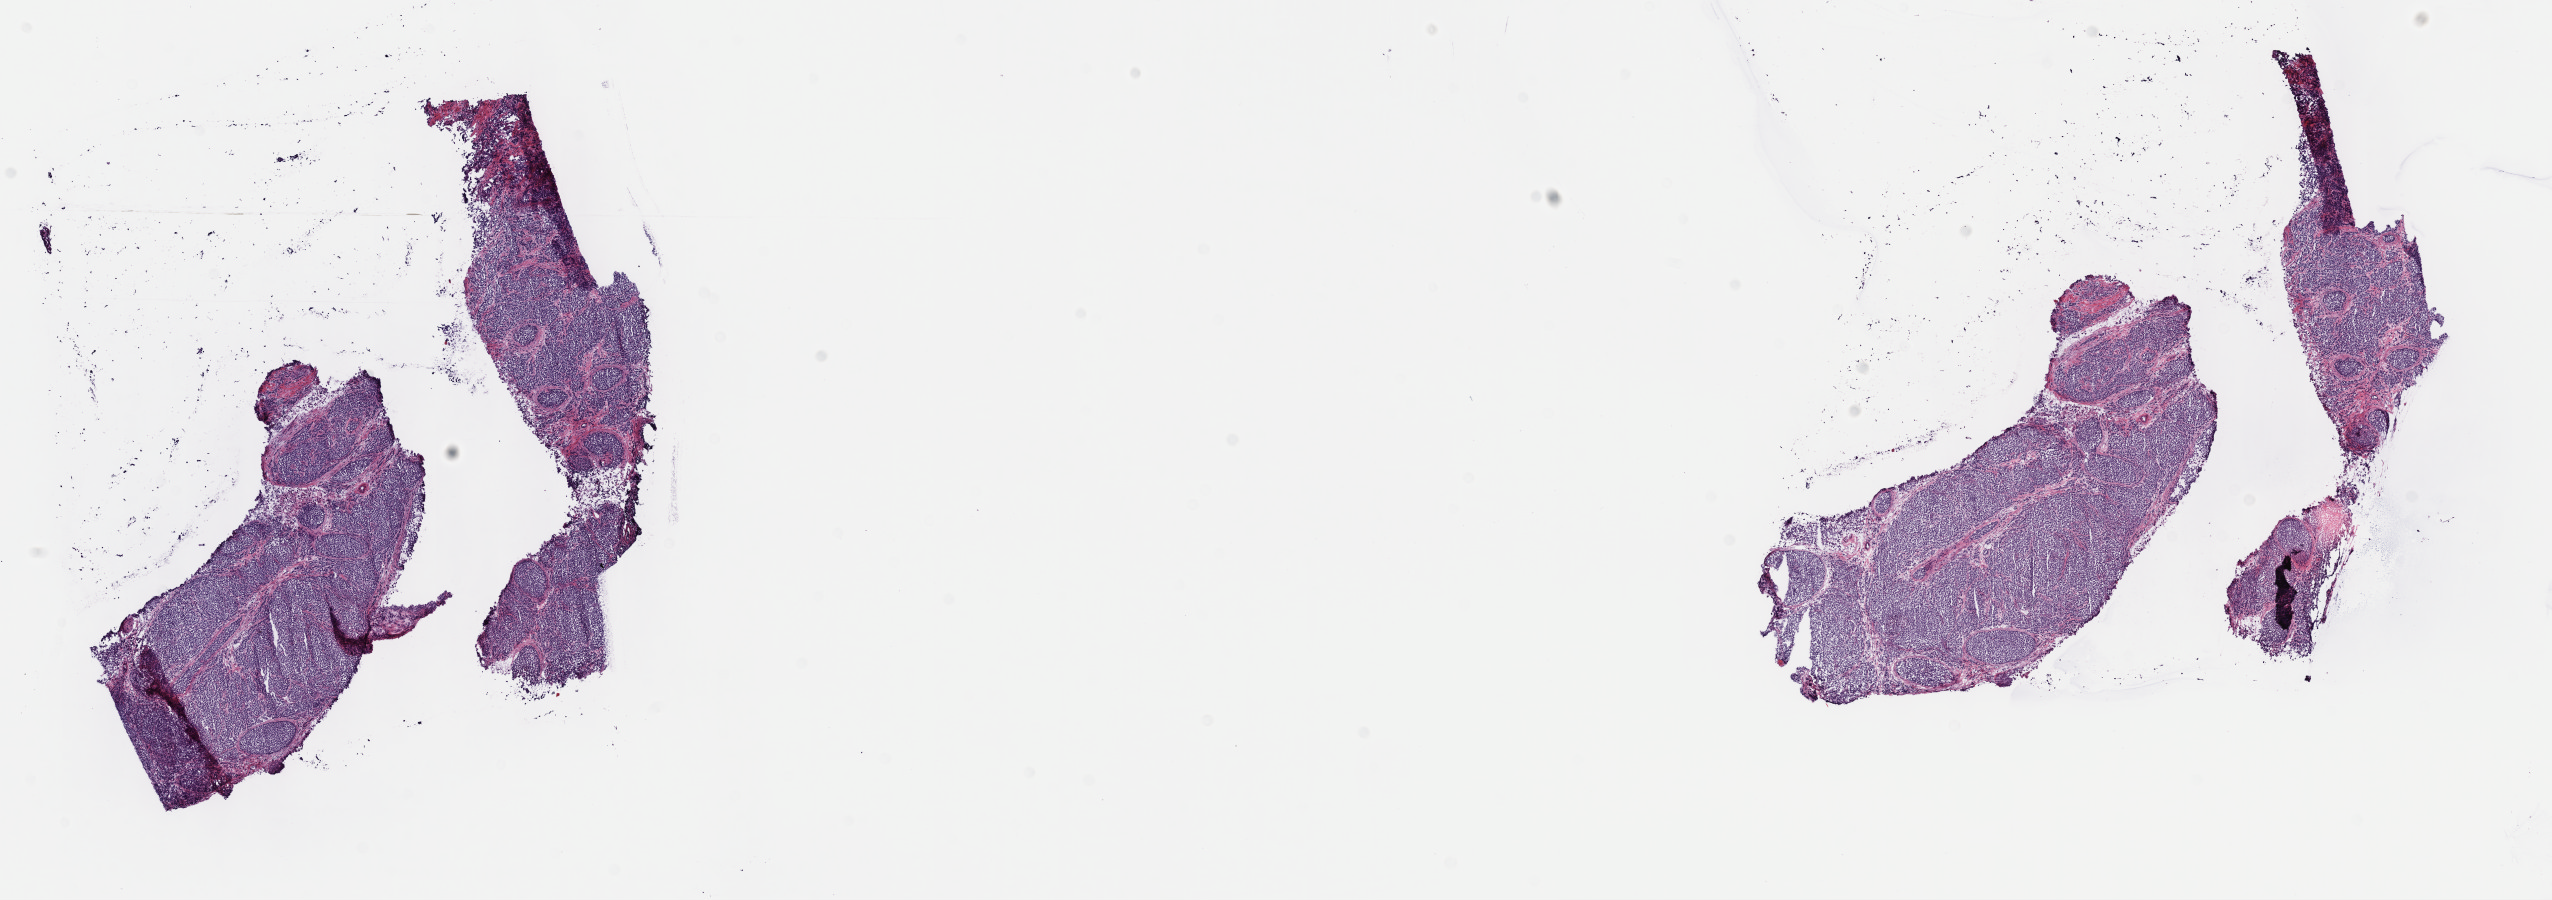
Hematoxylin and eosin (H&E) stained whole-slide image — low-resolution overview of the scanned area, about 20.6 x 7.3 mm. Frozen section from the top of the tissue portion. Sample: primary tumour, testis. Male, age 20 years at initial diagnosis. Pathologist review of this section (percent, as recorded): tumour cells 100%, tumour nuclei 80%, normal cells 0%, stromal cells 0%, necrosis 0%. Inflammatory infiltration, as recorded: lymphocyte infiltration 2%, monocyte infiltration 0%, neutrophil infiltration 0%.
* AJCC pathologic stage: I (4th edition)
* histologic diagnosis: Seminoma, NOS